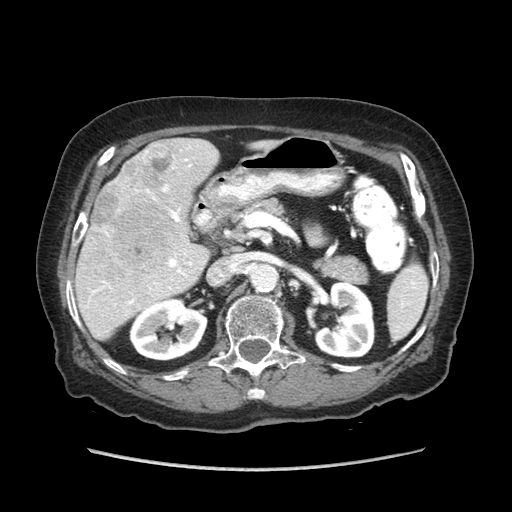
Contrast-enhanced abdominal CT (liver protocol), one axial slice; slice 37 of 89 in the series (ordered by position); reconstruction kernel STANDARD; soft-tissue window (W 400 / L 40 HU); 2.5 mm slice thickness; 512 × 512 image matrix, field of view 360 × 360 mm. From the clinical record (not read from this slice): diagnosis: hepatocellular carcinoma (patient treated with transarterial chemoembolisation; whether this scan precedes or follows treatment is not stated here); TNM stage (as recorded): Stage-IIIA; Child-Pugh class: A; tumour size: 11 cm.
Outlined on this slice (semi-automatically segmented with operator editing):
- liver parenchyma outside the tumour (the mass and vessels are separate outlines, so this box may not span the whole liver): bounding box (x1, y1, x2, y2) in pixels: (74, 138, 277, 340)
- mass: (91, 143, 172, 269)
- liver vessels: (91, 159, 192, 305)